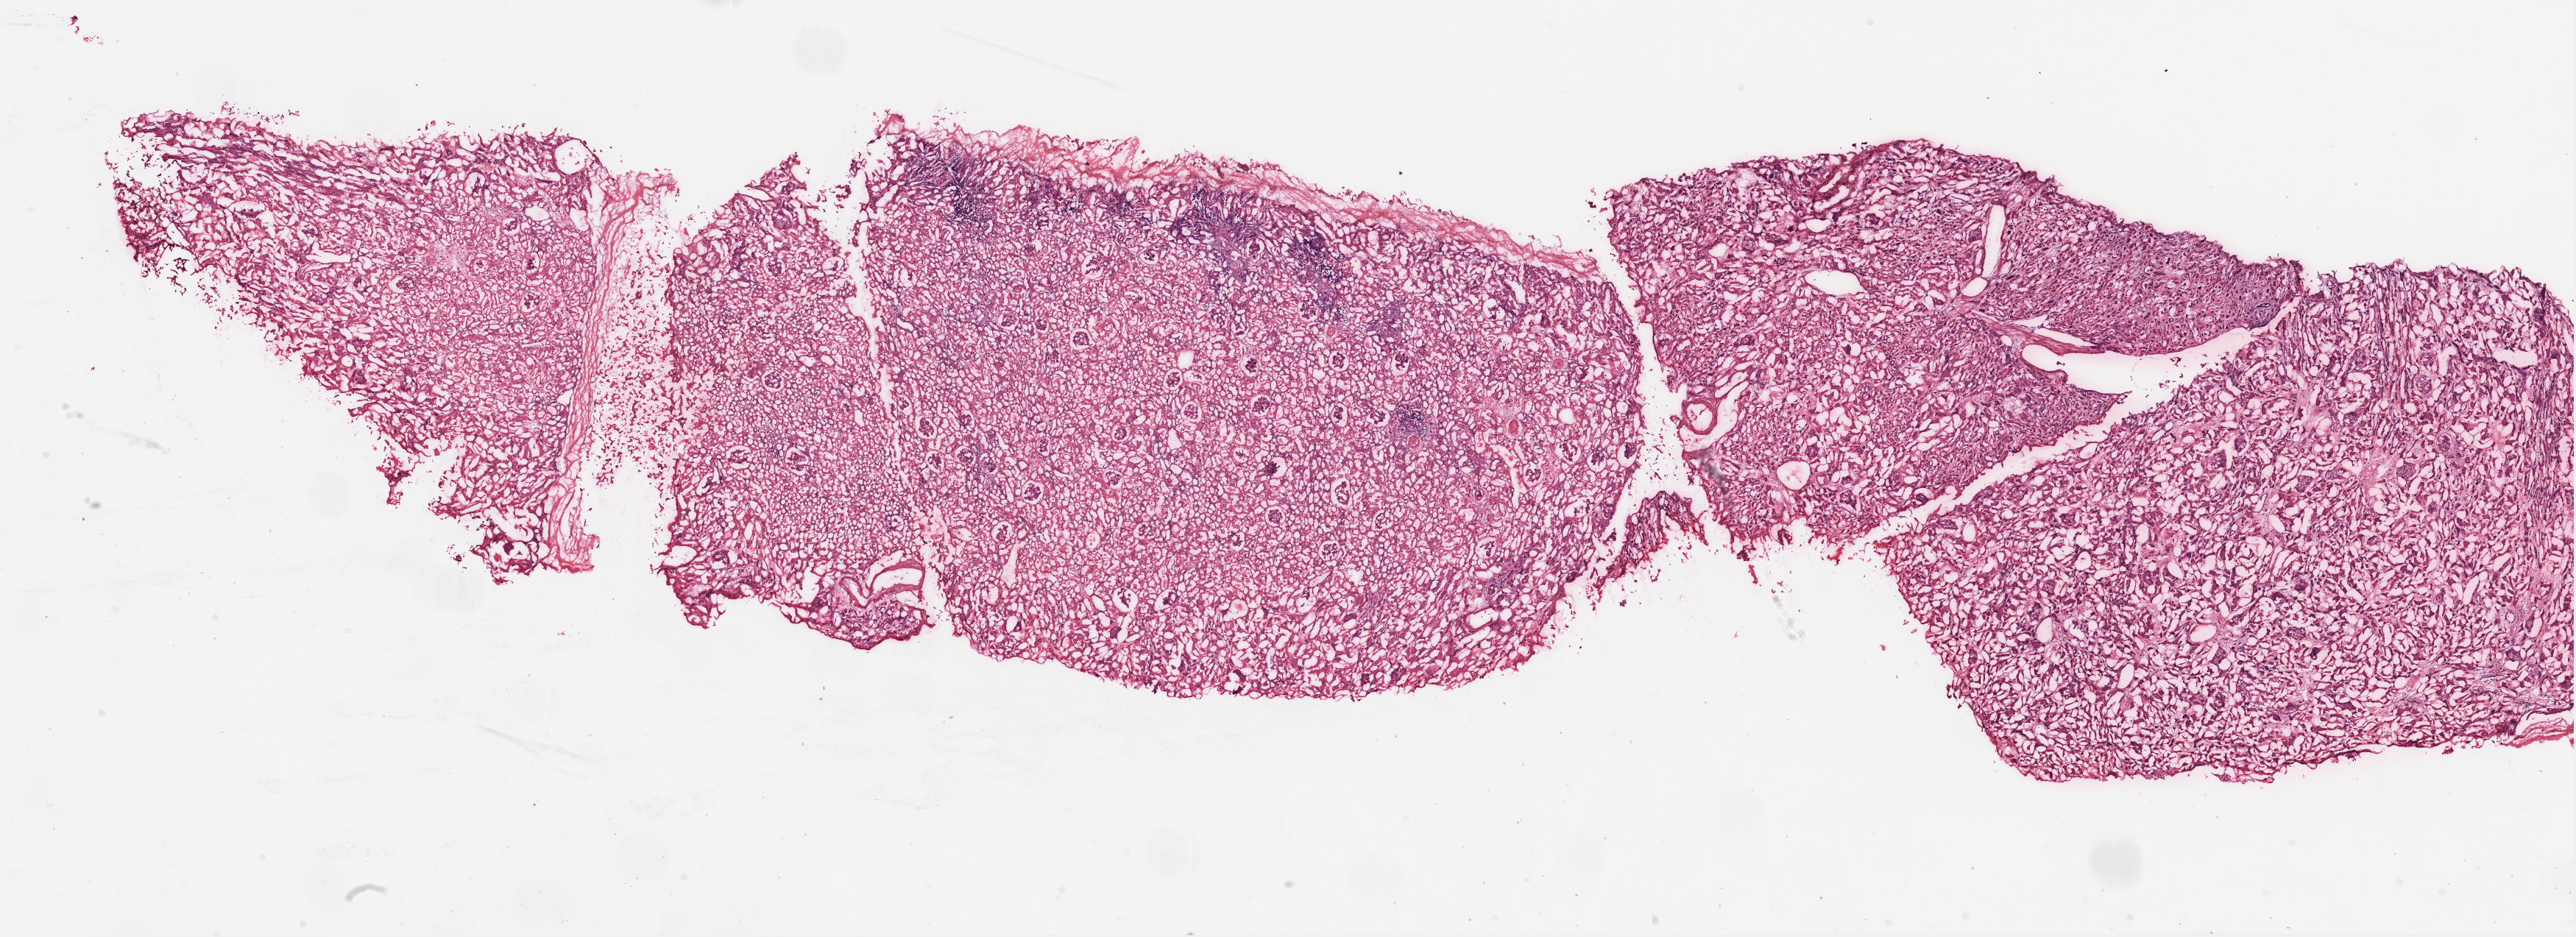
Hematoxylin and eosin (H&E) stained whole-slide image — whole scanned area (about 28.1 x 10.2 mm, slide scanned at 20x) shown as a low-resolution overview. Frozen section from the top of the tissue portion. Sample: solid tissue normal (non-tumour tissue), kidney. Female, age 71 years at initial diagnosis.
This section: solid tissue normal (non-tumour) sample from the same patient. Patient diagnosis: Clear cell adenocarcinoma, NOS.